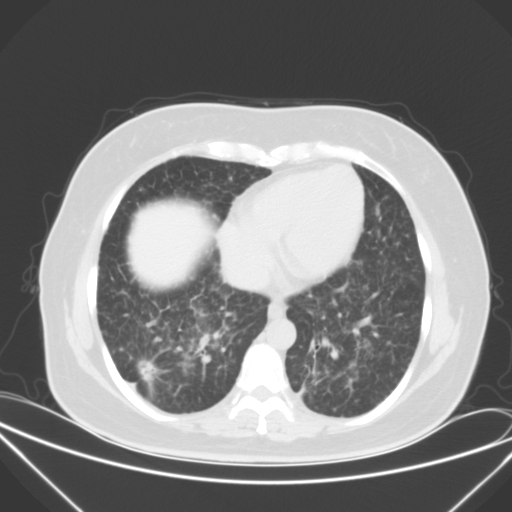
Chest CT, one axial slice; position 17 of 52 along the scan axis; 120 kVp; lung window (W 1500 / L -600 HU); 512 × 512 image matrix, field of view 386 × 386 mm. Patient: female, 50 years. From the clinical record (not read from this slice): clinical TNM (as recorded): T1c N0 M1a.
Structures marked on this image (bounding box drawn by a radiologist):
- lung tumour (recorded histology: adenocarcinoma): bounding box [x1, y1, x2, y2] px = [134, 357, 163, 394]